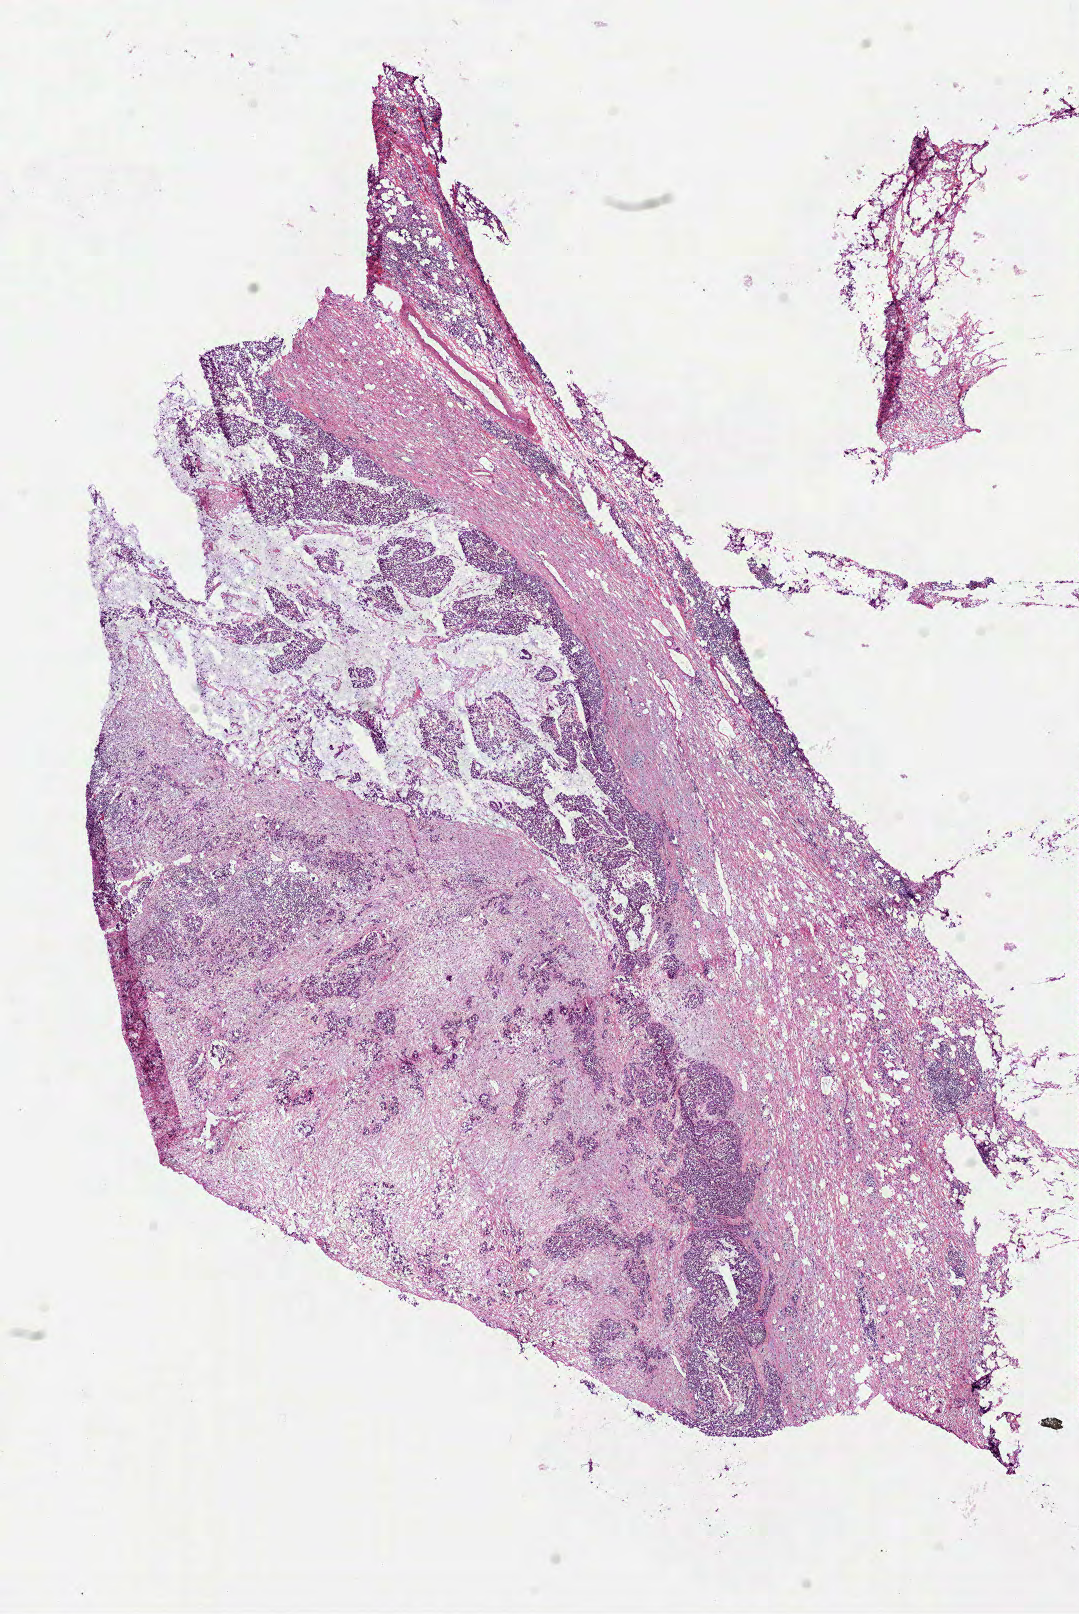
Digitized Hematoxylin and eosin (H&E) stained tissue section (whole slide), low-resolution overview of the scanned area, about 8.7 x 13.0 mm (slide scanned at 40x), frozen section, primary tumour sample from the colon. Patient: male, age at initial diagnosis 47 years. Slide review estimates, as recorded: tumour cells 40%, tumour nuclei 75%, normal cells 0%, stromal cells 60%, necrosis 0%.
- pathologic diagnosis: Mucinous adenocarcinoma (ascending colon)
- AJCC pathologic stage: IIIC